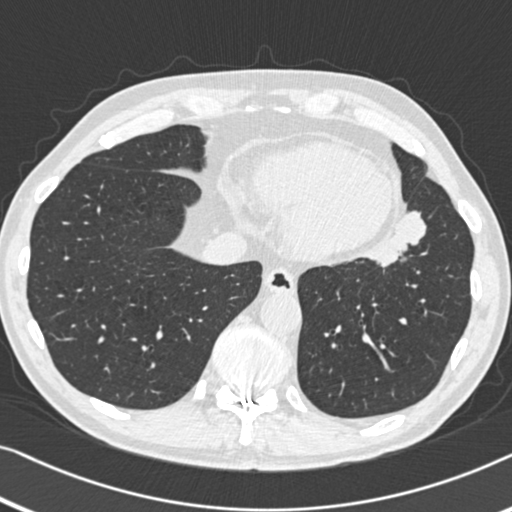
Low-dose screening chest CT, one axial slice; position 130 of 383 along the scan axis; reconstruction kernel B30f; lung window (W 1500 / L -600 HU); 1 mm slice thickness; 512 × 512 image matrix.
Structures marked on this image (manually delineated by an expert):
- lesion 1 (tumor, upper lobe of left lung): bounding box <376,211,426,267> (left, top, right, bottom; pixels)